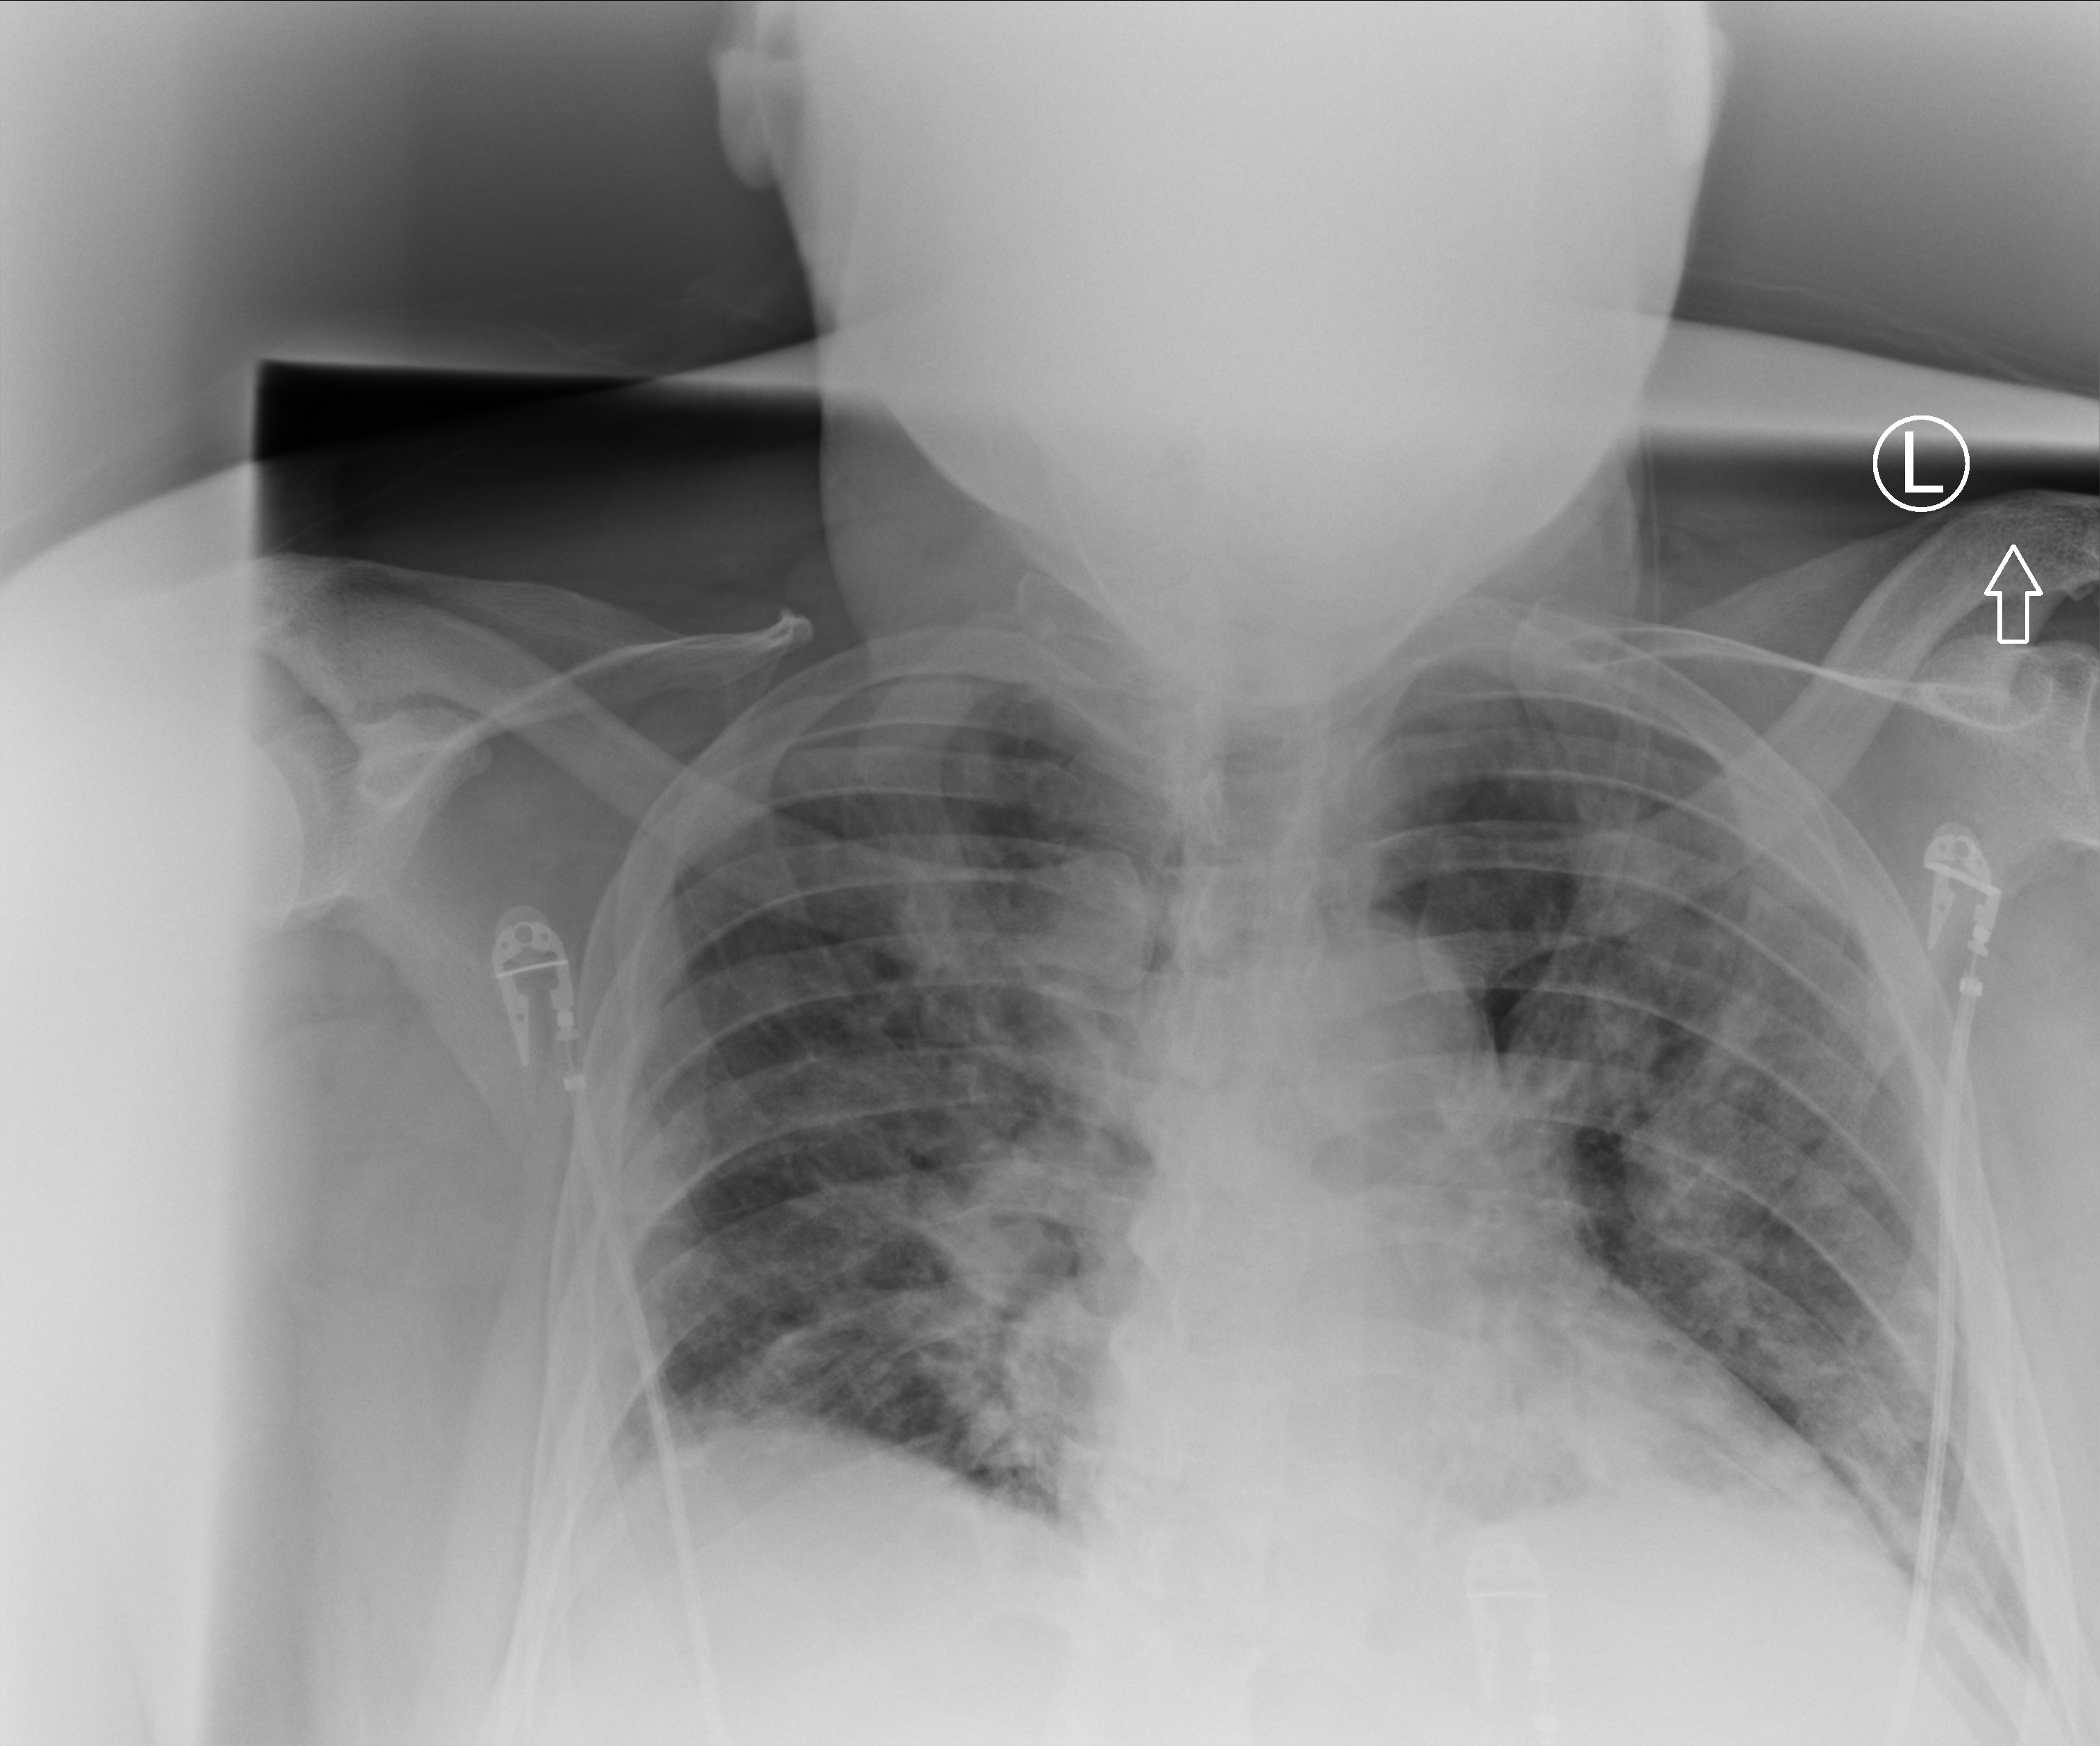
Bedside chest radiograph (computed radiography), anteroposterior (AP) projection. Male patient hospitalised with COVID-19, age 60–74 years.
Admission-level facts for this patient (not findings on this image; timing relative to this image not recorded): hypertension (admission record): yes; admitted to intensive care during this hospital stay: no; mechanically ventilated during this hospital stay: no.